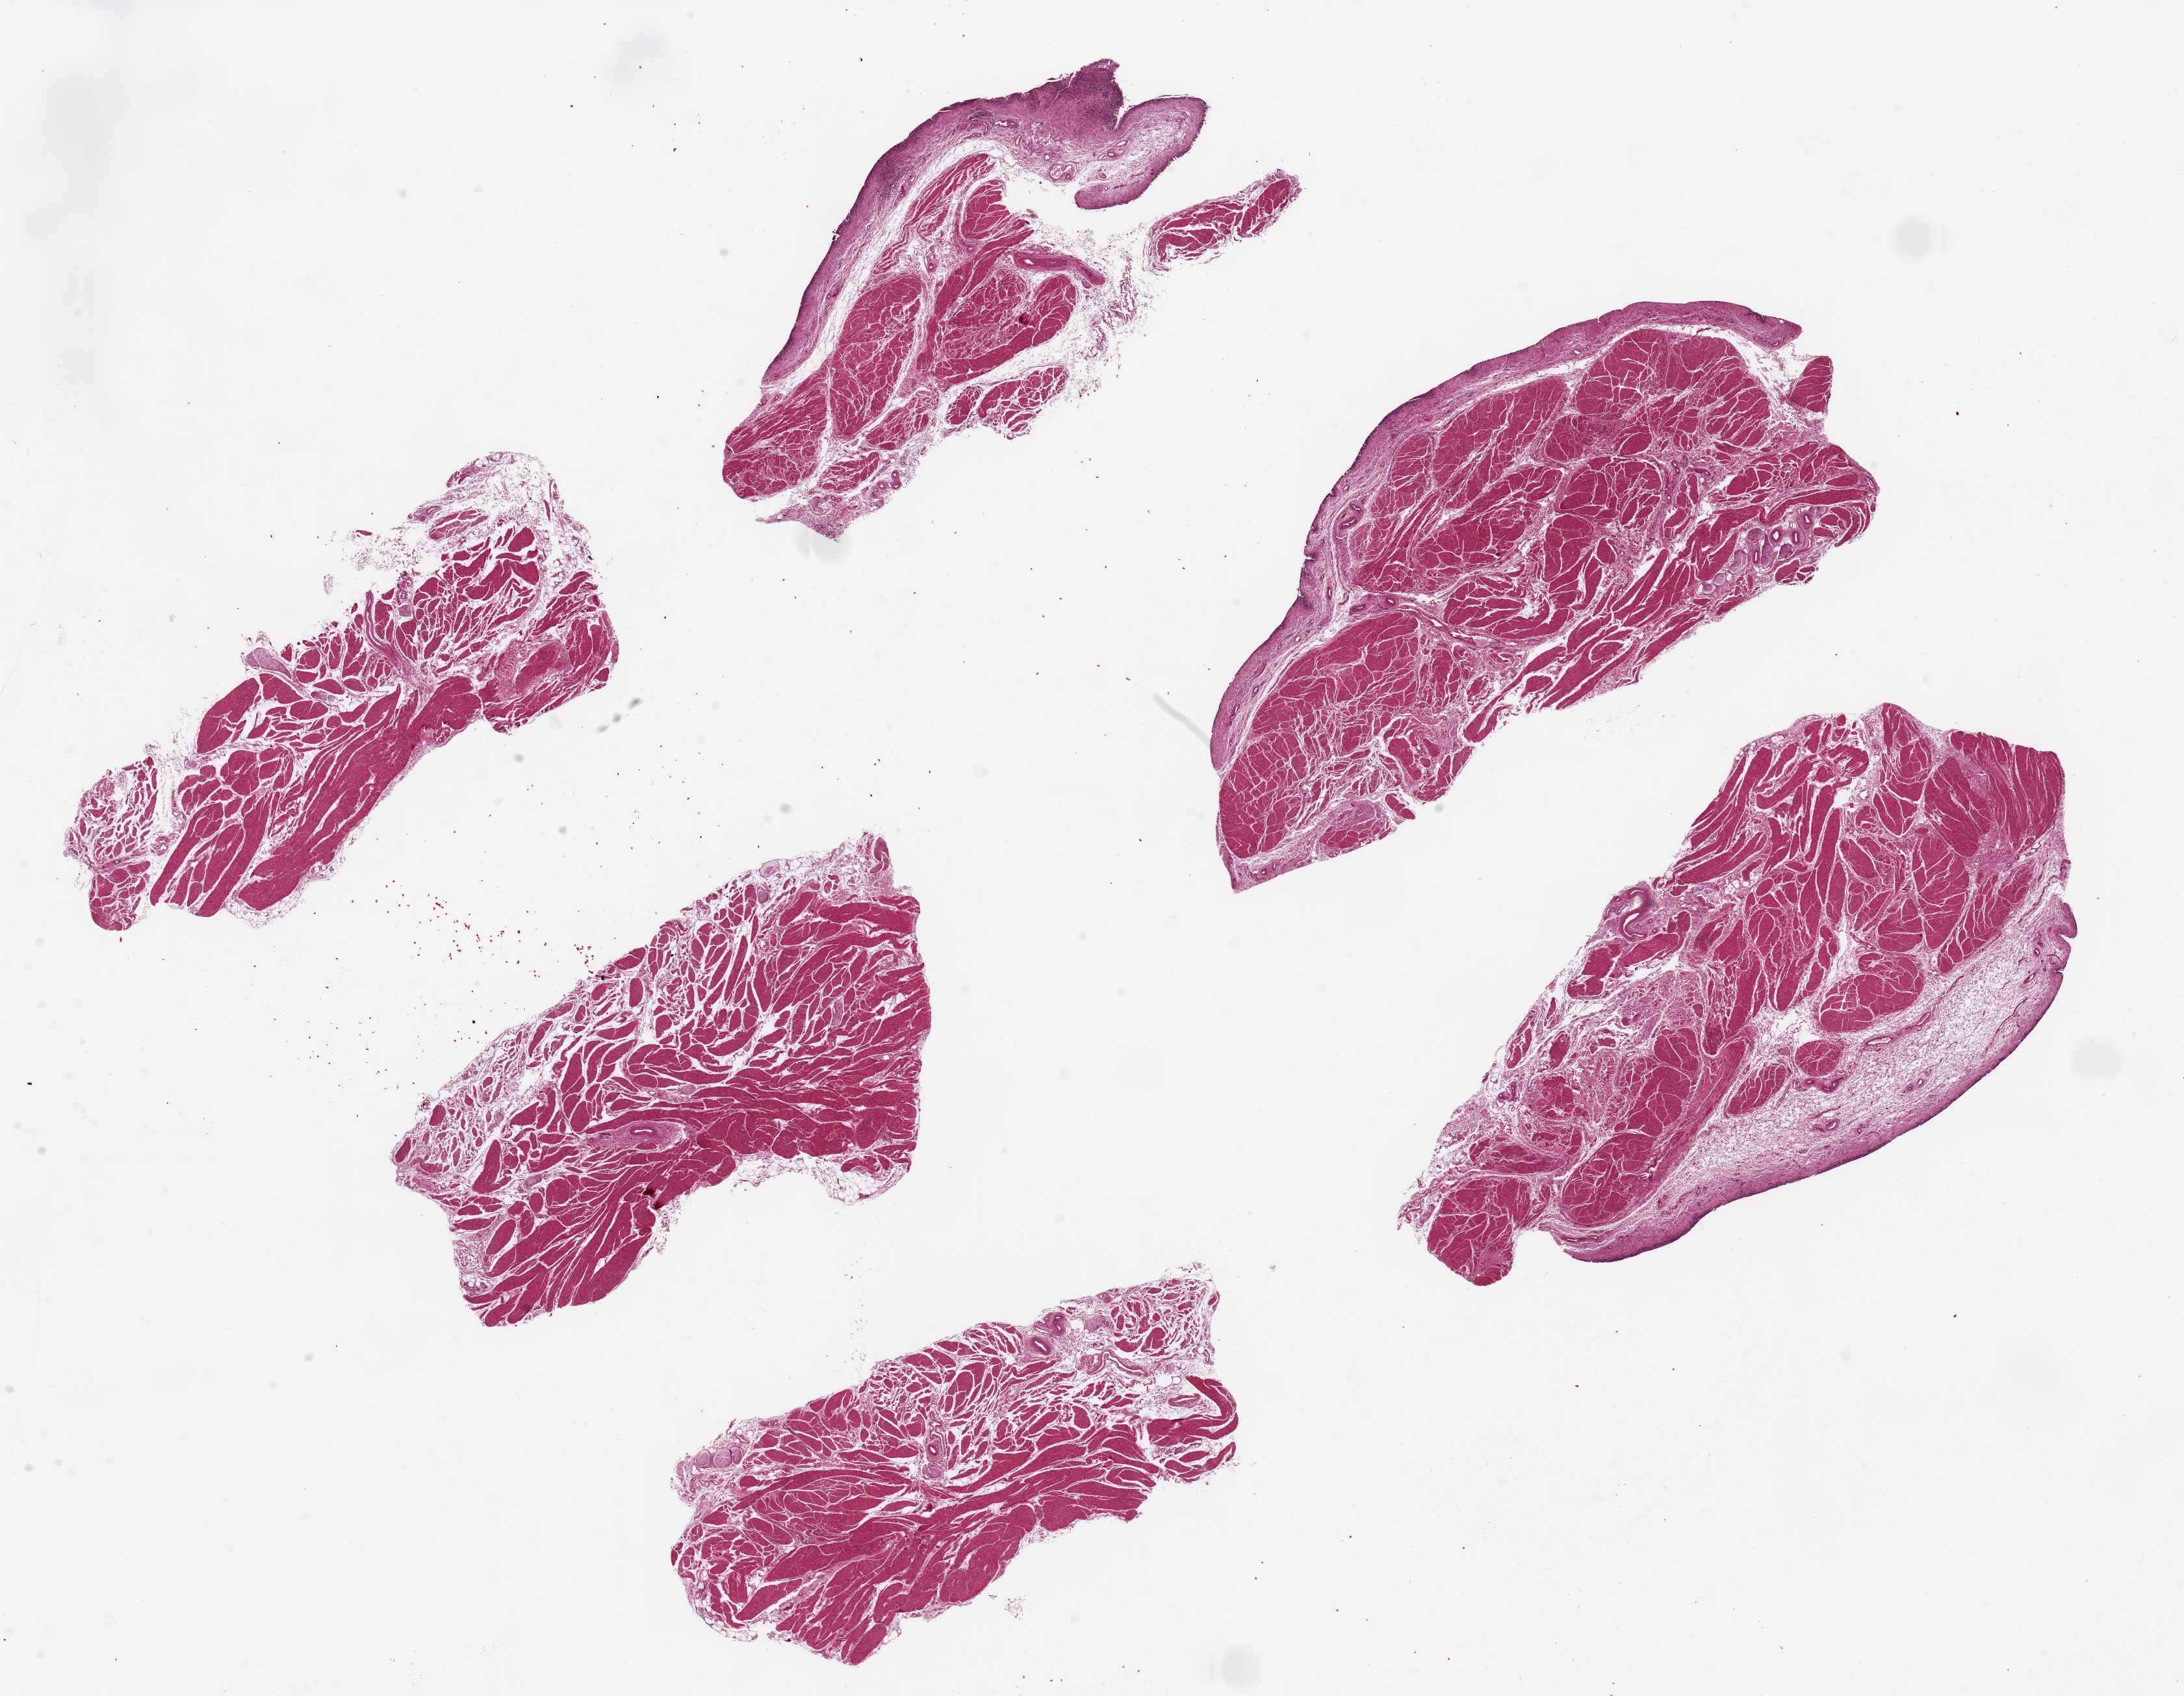
Haematoxylin and eosin whole-slide image — shown as a low-resolution overview of the whole scanned area (about 26.6 x 20.6 mm), PAXgene-fixed, paraffin-embedded tissue, target tissue: urinary bladder, tissue donor sample. Donor sex: female.
- review note (as recorded): 6 pieces up to 9.6x4.8 mm; 3 have mucosa but largely sloughed, 3 only muscularis